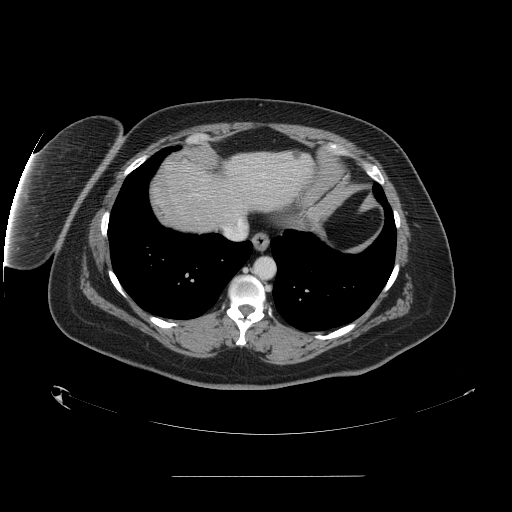
Contrast-enhanced abdominal CT, one axial slice. Slice 139 of 164 in the series (ordered by position). 120 kVp. Intravenous contrast given. Soft-tissue window (W 400 / L 40 HU). 2.5 mm slice thickness. 512 × 512 image matrix, field of view 495 × 495 mm. Female patient, age 52 years. From the clinical record (not read from this slice): diagnosis: colorectal cancer liver metastases, imaged before liver resection; multiple liver metastases: yes; largest metastasis: 3.5 cm; disease in both lobes: no.
Structures marked on this image (outlined manually by an expert reader):
- hepatic veins: bounding box (x1, y1, x2, y2) in pixels: (223, 214, 246, 240)
- liver: (159, 151, 313, 232)
- planned liver remnant (the part of the liver to remain after resection): (181, 151, 313, 225)
- liver metastasis: (295, 156, 300, 159)